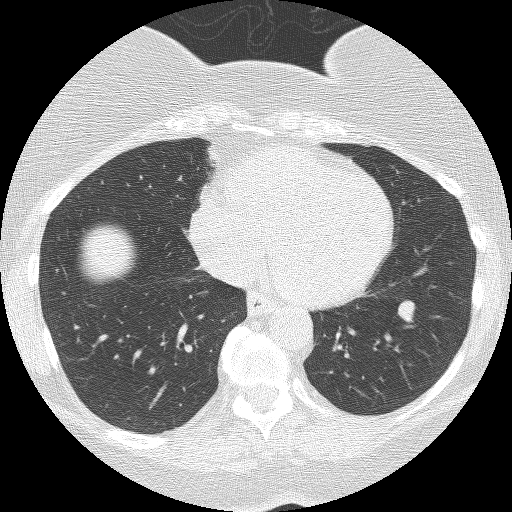
Chest CT (low-dose screening protocol), one axial image, third annual screen, lung window (W 1500 / L -600 HU), lung (sharp) reconstruction kernel (BONE), slice 110 of 167 in the series. Female, age 55 years at enrolment. Former smoker at enrolment.
Lesion marked by an expert reader, bounding box (x1, y1, x2, y2) in pixels: (381, 289, 430, 335). The screening reader recorded 3 non-calcified nodules or masses ≥4 mm on this exam (right lower lobe, right lower lobe, left lower lobe); which of them this box marks is not recorded. Official screen result: positive, no significant change: stable abnormalities potentially related to lung cancer, unchanged since the prior screening exam. Later outcome: lung cancer diagnosed 356 days after this screen — carcinoid tumor, NOS, left lower lobe, carcinoid, stage not assessed, 10 mm at pathology.